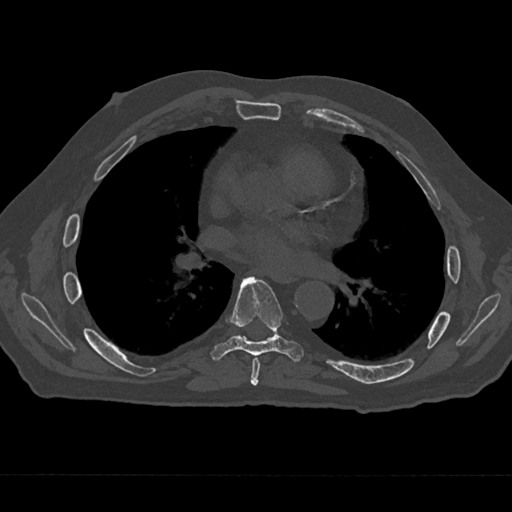
CT including the spine, one axial slice. Position 374 of 797 along the scan axis. Reconstruction kernel Br40s/3. 120 kVp. Bone window (W 1800 / L 400 HU). 0.5 mm slice thickness. 512 × 512 image matrix, field of view 377 × 377 mm. Patient: male, 75 years. From the clinical record (not read from this slice): primary cancer: renal.
Annotated regions visible in this slice (semi-automatically segmented with operator editing):
- T6 vertebra: bounding box [x1, y1, x2, y2] px = [250, 358, 260, 386]
- T7 vertebra: [210, 276, 304, 362]